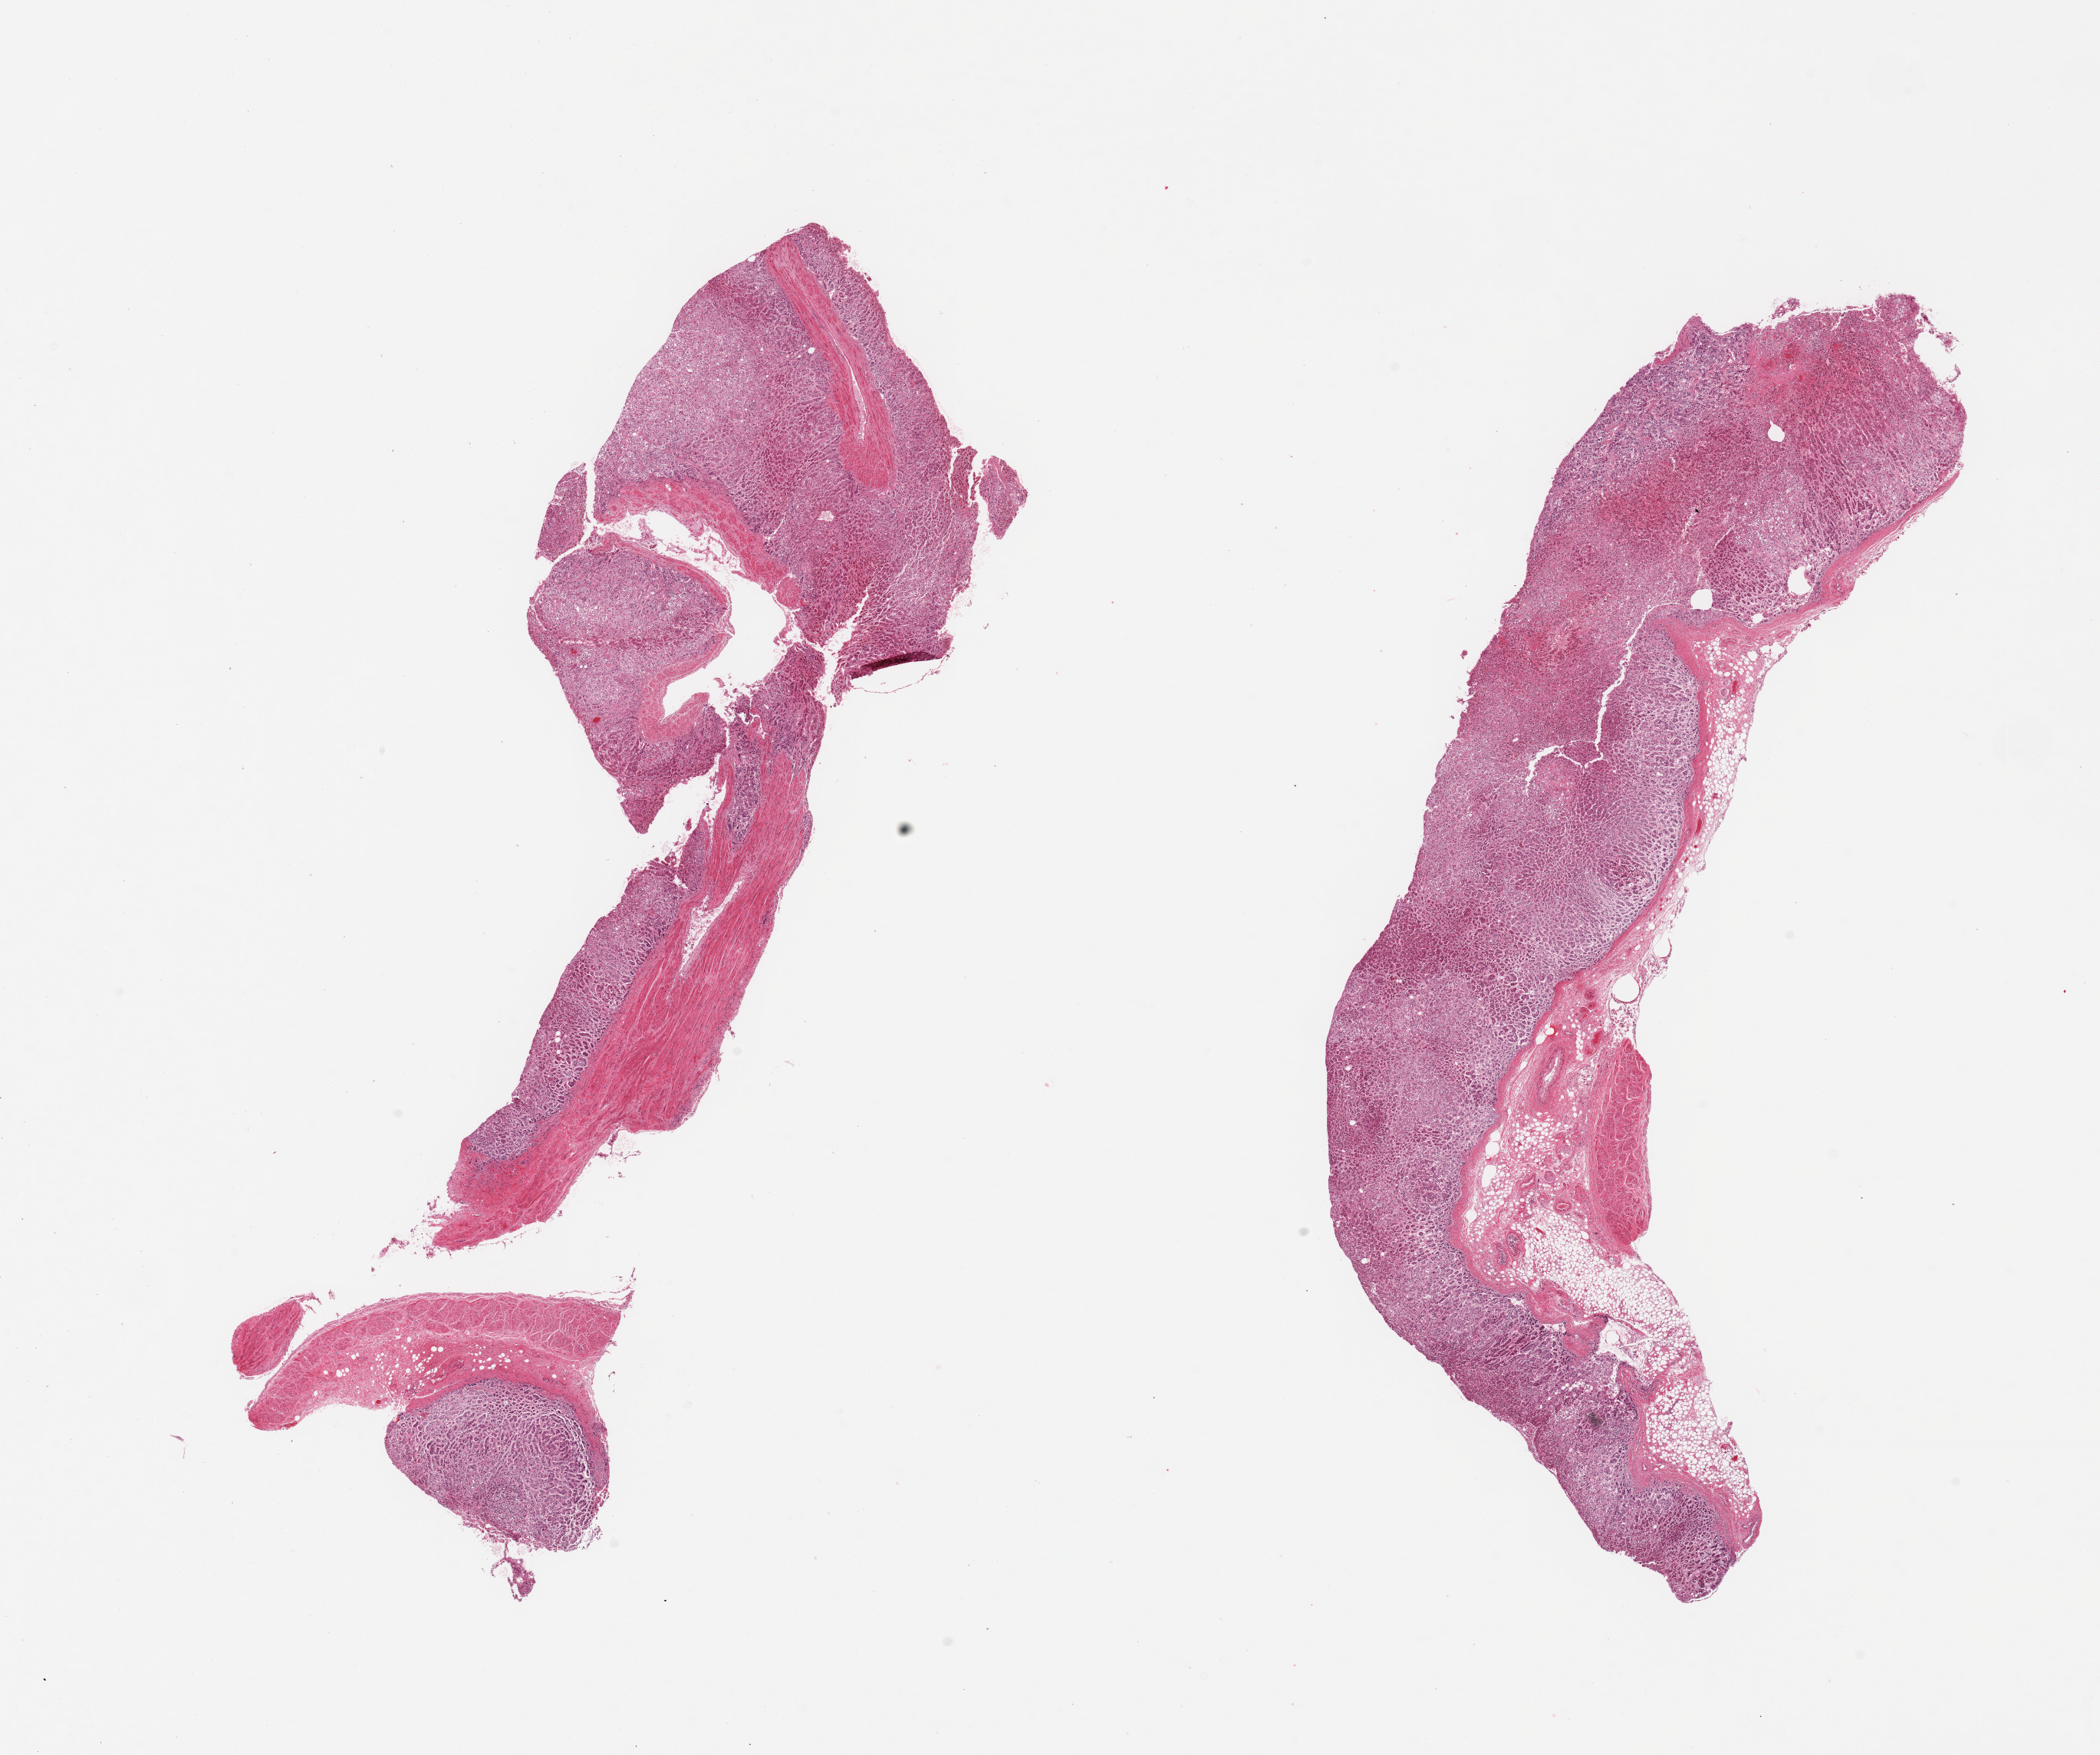
Digitized hematoxylin and eosin (H&E)-stained section — a low-resolution overview of the entire scanned area, about 21.7 x 18.1 mm; PAXgene-fixed, paraffin-embedded tissue; section of adrenal gland (target tissue); tissue donor sample. Male donor.
Pathologist's review note for this sample: 2 pieces; moderately autolyzed adrenal cortex and medulla; one contains 15% to 20% fibrous tissue other ~20% external fat.